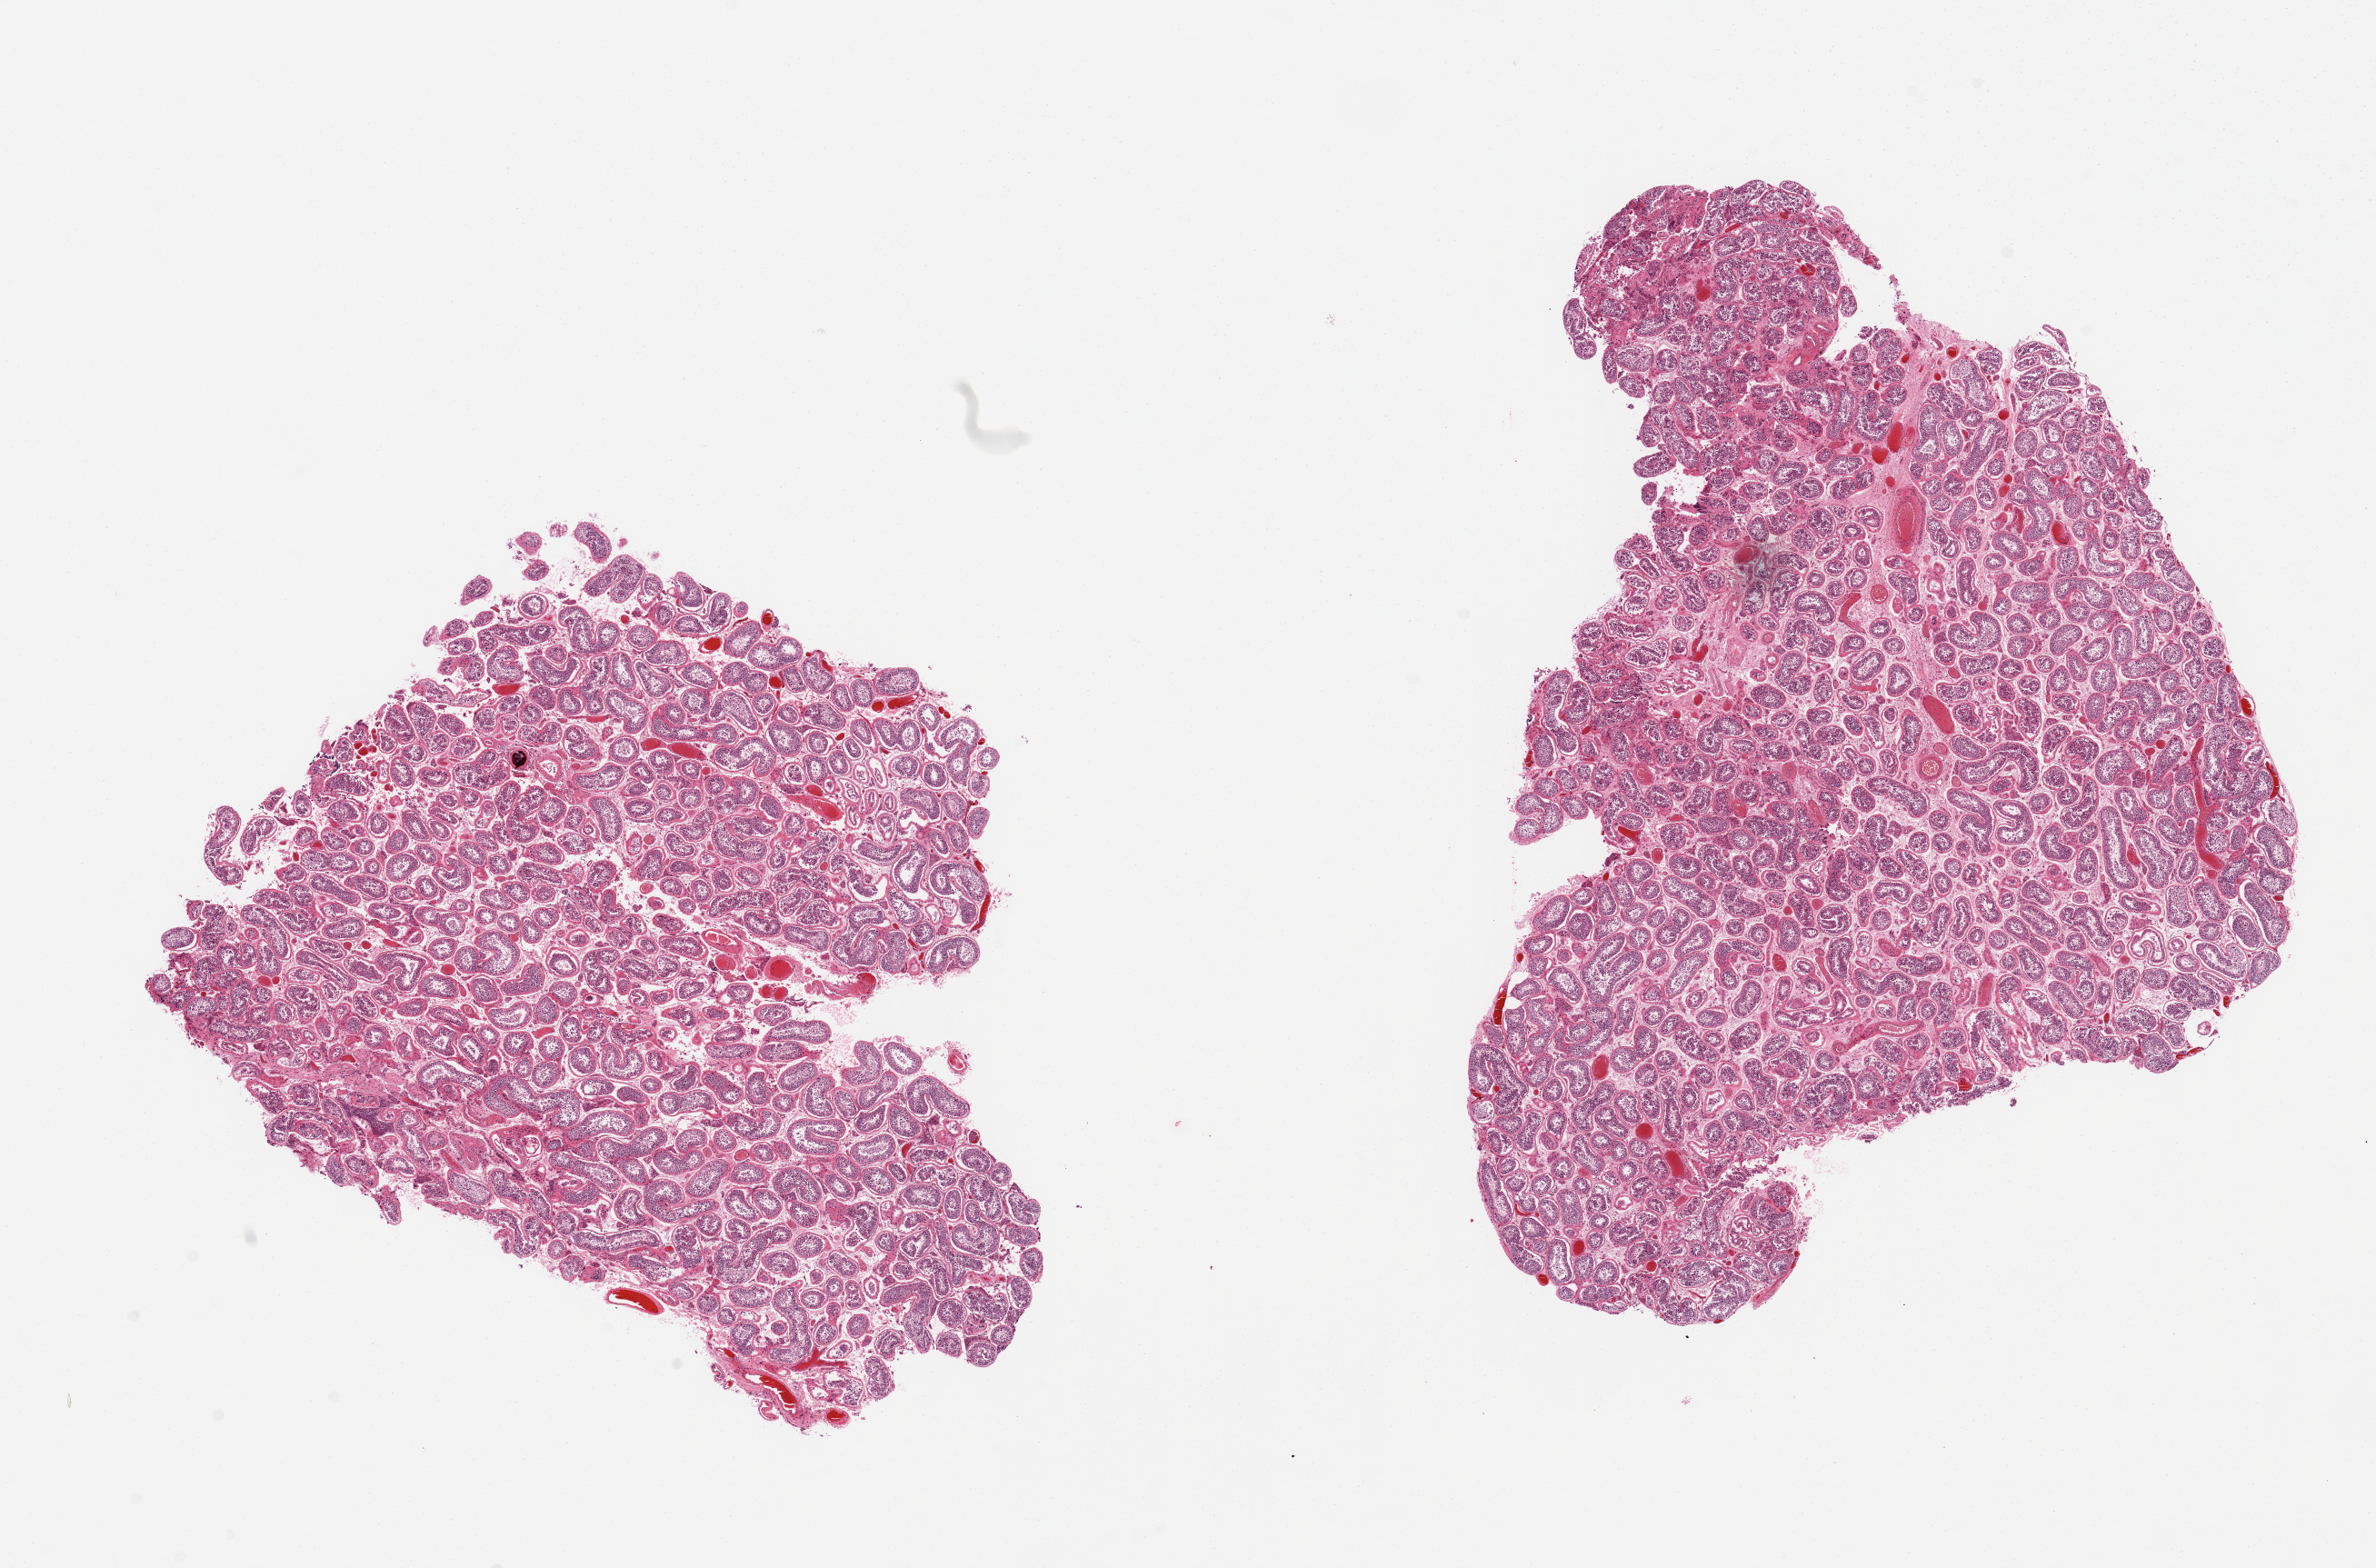
Haematoxylin and eosin whole-slide image, brightfield — low-resolution overview of the scanned area, about 20.7 x 13.6 mm (slide scanned at 20x); PAXgene-fixed, paraffin-embedded tissue; sampled site (target tissue): testis; tissue donor sample. Donor: male.
Reviewer comment on this tissue sample: 2 pieces; spermatogenesis.